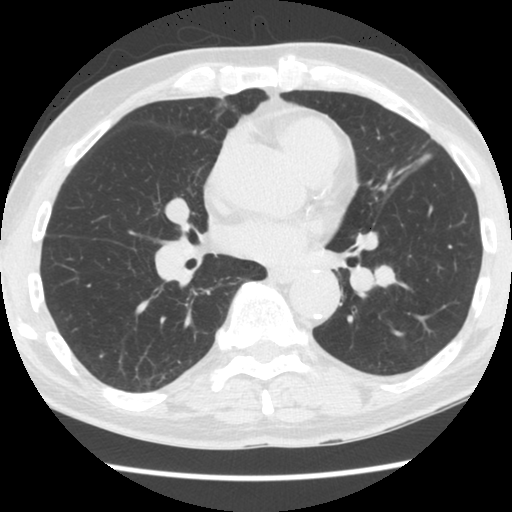
Low-dose screening chest CT, one axial slice. Position 78 of 174 along the scan axis. Lung window (W 1500 / L -600 HU). 512 × 512 image matrix.
Annotated regions visible in this slice (manually delineated by an expert):
- lesion 1 (tumor, lower lobe of left lung): bounding box [x1, y1, x2, y2] px = [375, 266, 395, 286]